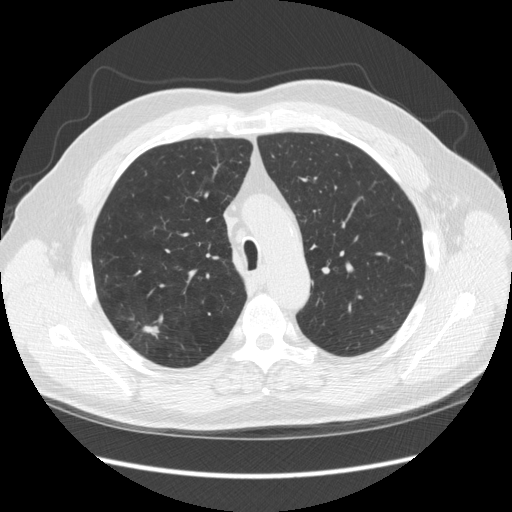
Axial slice from a low-dose chest CT screening exam. Third annual screen. Lung window (W 1500 / L -600 HU). 120 kVp. Slice 68 of 248 in the series. 512 × 512 image matrix. Male, age 64 years at enrolment. Former smoker at enrolment.
Expert reader's lesion annotation, bounding box [x1, y1, x2, y2] px = [117, 314, 170, 358]. The screening reader recorded 4 non-calcified nodules or masses ≥4 mm on this exam (right upper lobe, right upper lobe, right upper lobe, right upper lobe); which of them this box marks is not recorded. Later outcome: lung cancer diagnosed 15 days after this screen — adenocarcinoma, NOS, right upper lobe, moderately differentiated (G2), stage IA (AJCC 6th edition), 14 mm at pathology.